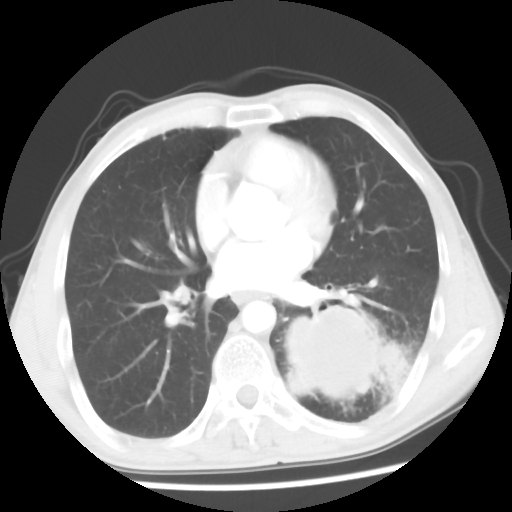
Chest CT, one axial slice; slice 26 of 56 in the series (ordered by position); 120 kVp; lung window (W 1500 / L -600 HU); 512 × 512 image matrix. Male patient, age 60 years. From the clinical record (not read from this slice): clinical TNM (as recorded): T4 N0 M0.
Annotated regions visible in this slice (bounding box drawn by a radiologist):
- lung tumour (recorded histology: squamous cell carcinoma): bounding box <267,294,412,427> (left, top, right, bottom; pixels)